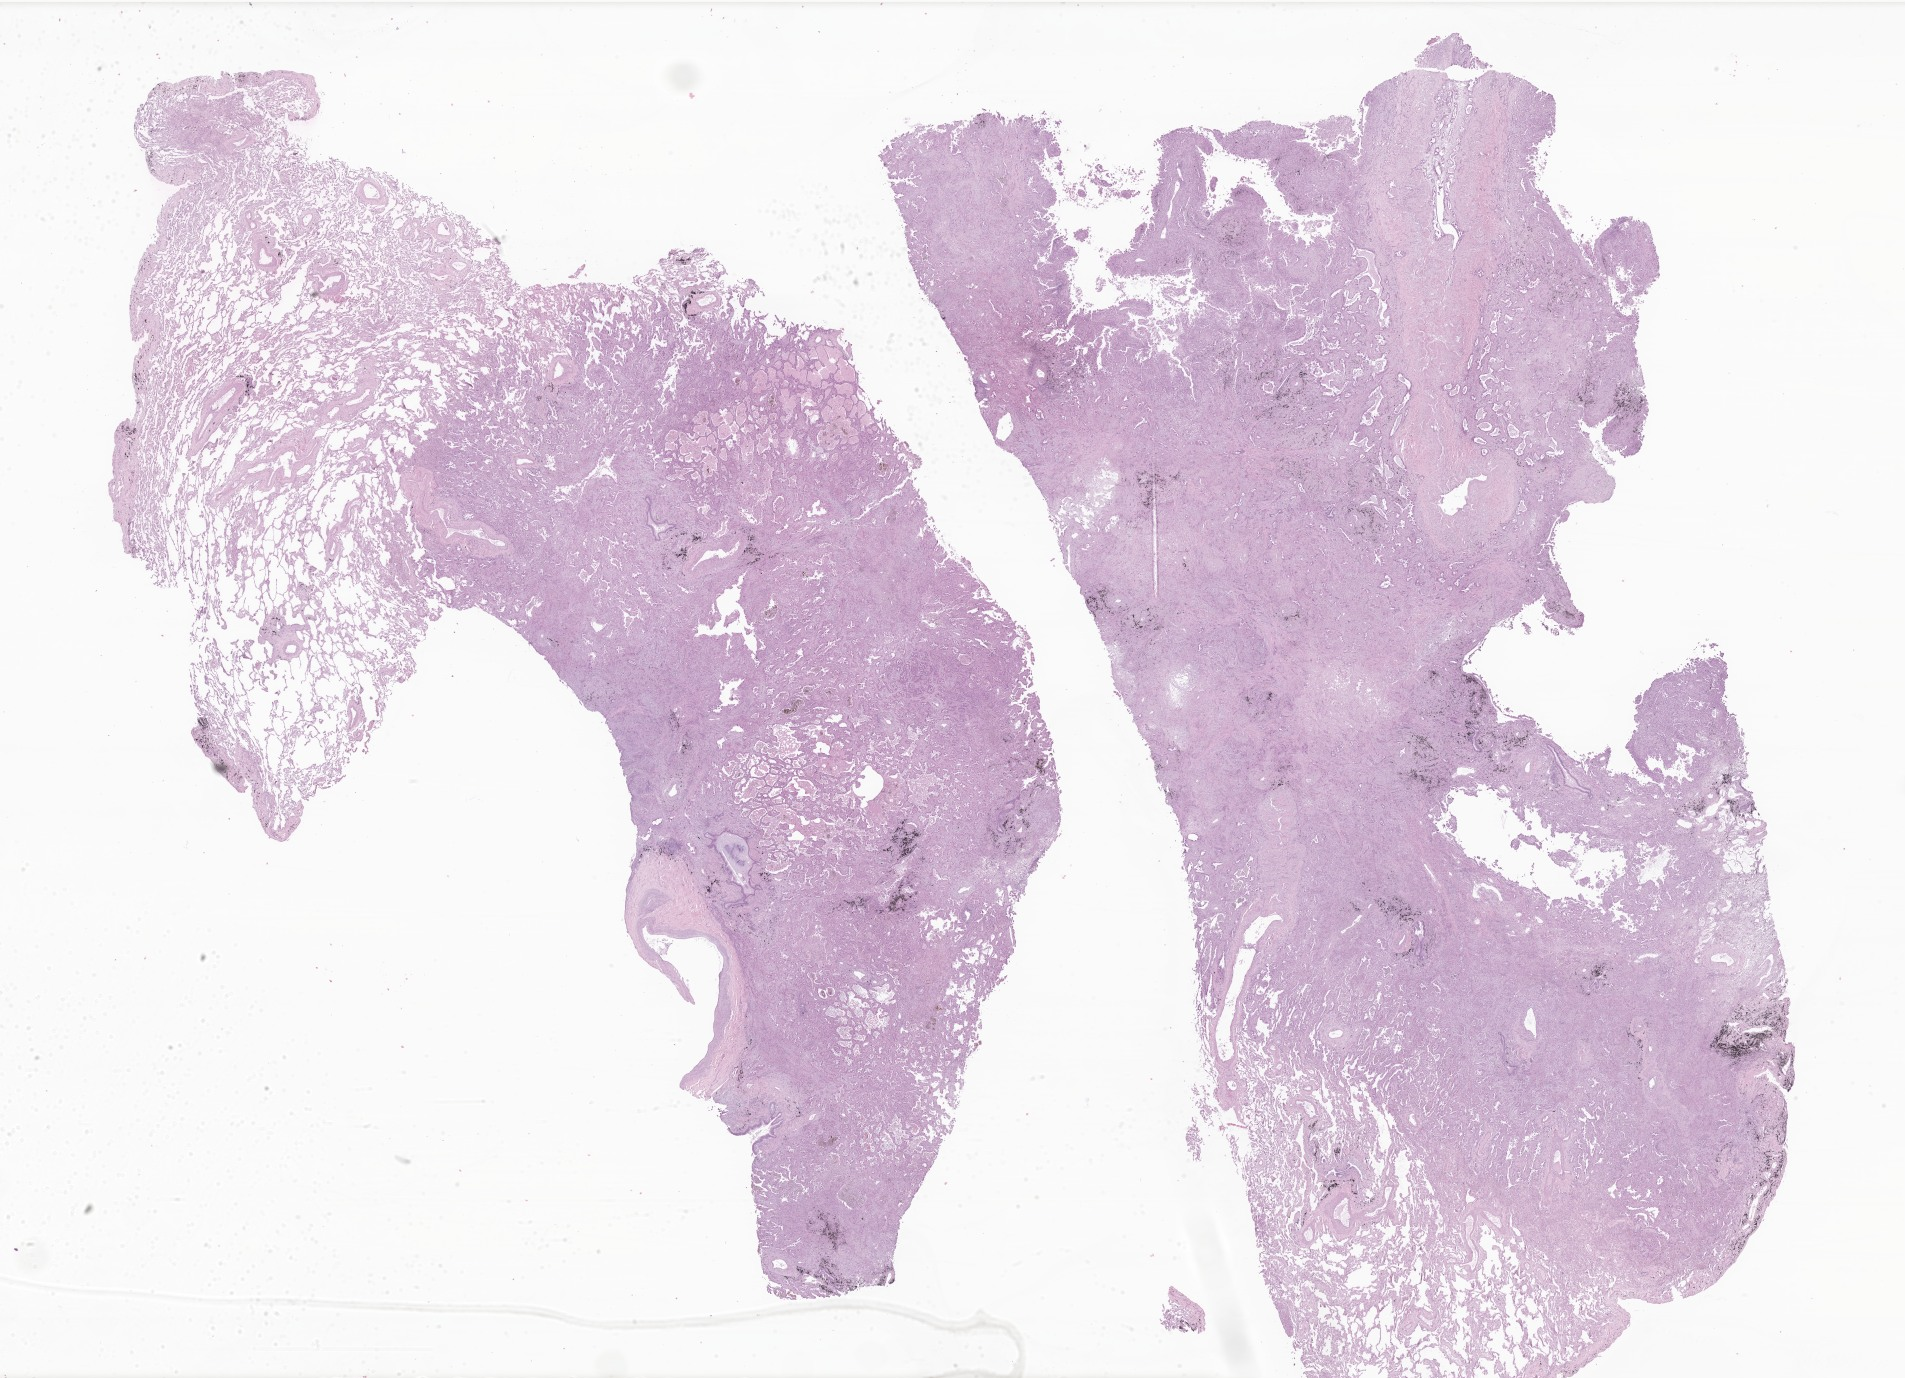
Digitized haematoxylin and eosin-stained section — a low-resolution overview of the entire scanned area, about 32.1 x 23.2 mm, tumor tissue, anatomic site: lung. Patient male; aged 69.
• histologic diagnosis: Non-small cell carcinoma